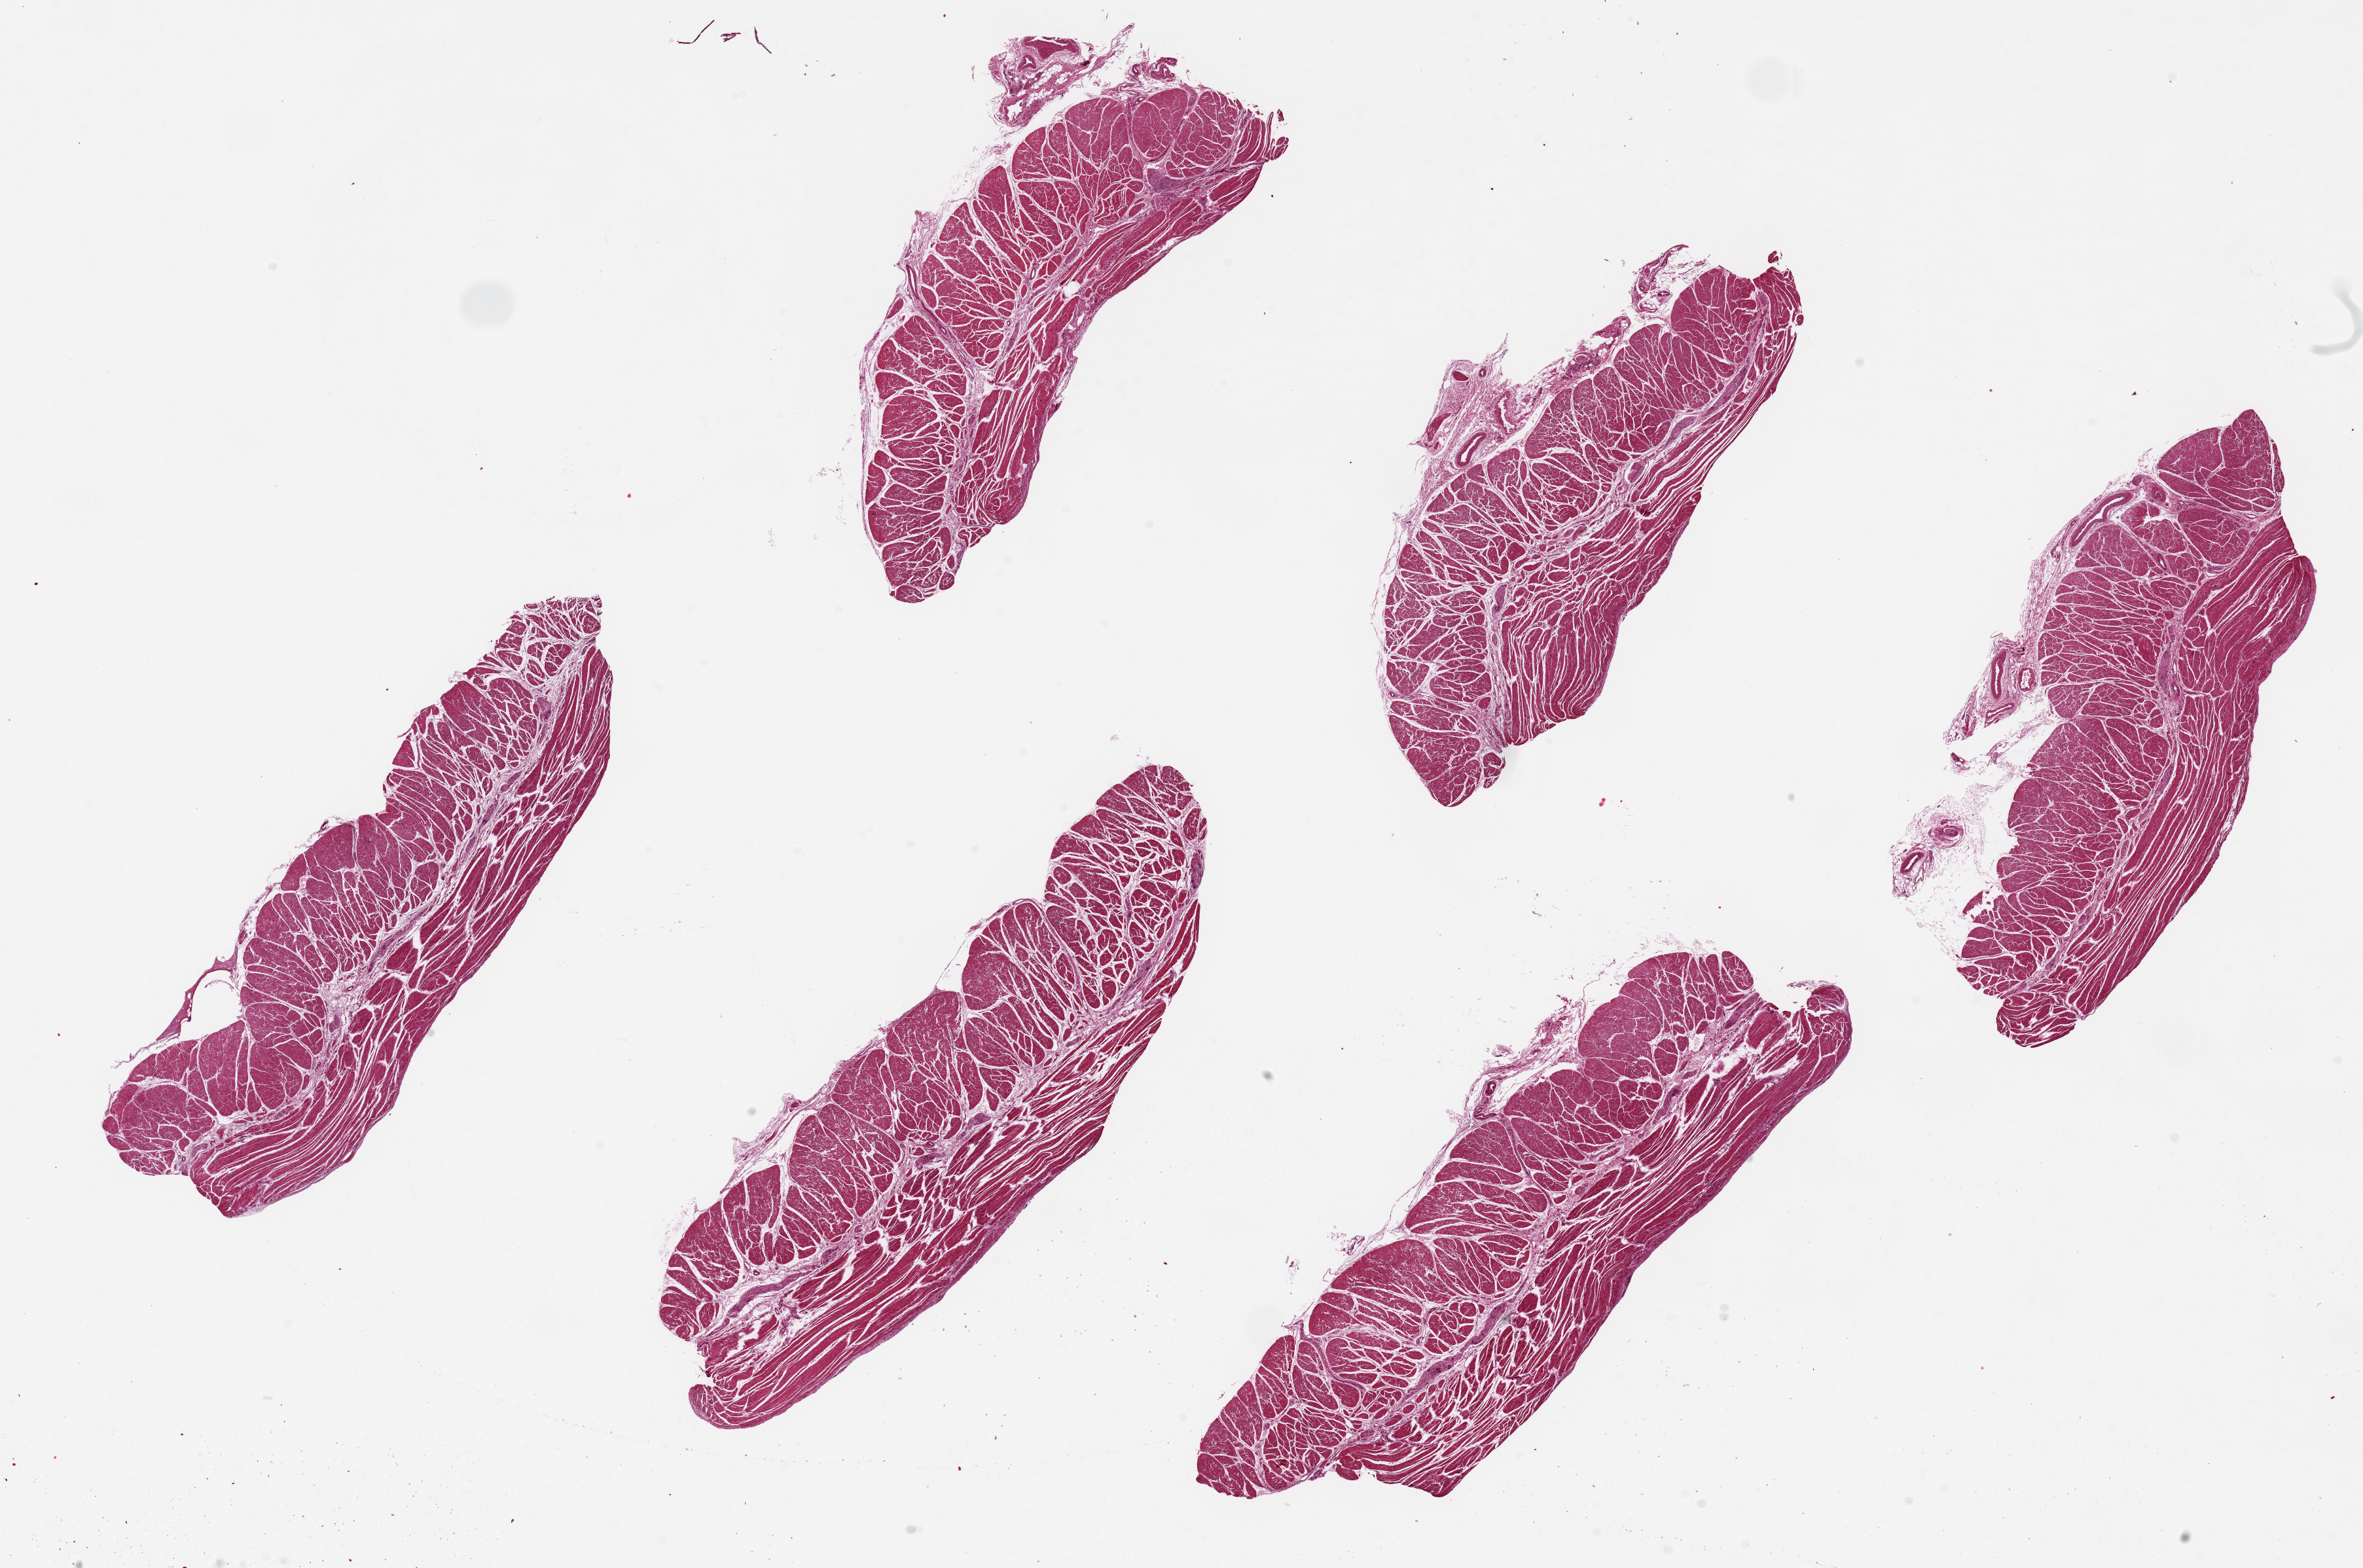
H&E whole-slide image, whole scanned area (about 28.5 x 18.9 mm, from a 20x scan) shown as a low-resolution overview; PAXgene-fixed, paraffin-embedded tissue; sampled site (target tissue): esophageal muscle; tissue donor sample.
Pathologist's review note for this sample: 6 pieces.